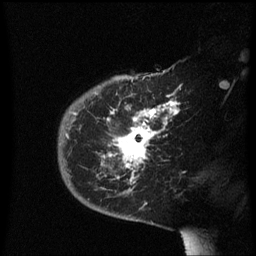
Breast MRI (dynamic contrast-enhanced), one sagittal slice. Slice 43 of 60 in the series (ordered by position). Dynamic contrast-enhanced series, image 2 of 3 at this slice position (ordered by acquisition). 1.5 T. TE 4.2 ms, TR 8.4 ms. 256 × 256 image matrix. Female patient, age 38 years. Case-level facts recorded for this patient, not image findings: setting: breast cancer imaged before/during neoadjuvant chemotherapy; receptor status: HER2-positive.
Annotated regions visible in this slice (semi-automatically segmented with operator editing):
- analysis volume of interest (the breast-tissue region the enhancement analysis was run in; not a lesion): bounding box [x1, y1, x2, y2] px = [58, 78, 182, 213]
- tumour enhancement mask (voxels above the 70 % enhancement threshold inside the analysis volume of interest): [67, 100, 179, 185]